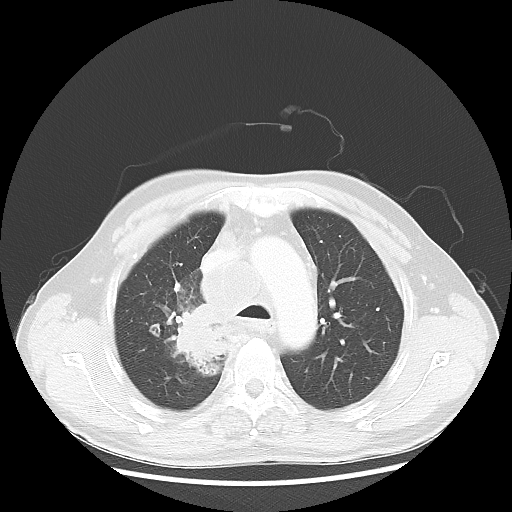
Chest CT, one axial slice; slice 42 of 60 in the series (ordered by position); reconstruction kernel LUNG; lung window (W 1500 / L -600 HU); 512 × 512 image matrix, field of view 382 × 382 mm. Patient: male, 64 years. From the clinical record (not read from this slice): clinical TNM (as recorded): T3 N3 M0.
Annotated regions visible in this slice (bounding box drawn by a radiologist):
- lung tumour (recorded histology: small cell carcinoma): bounding box <168,302,246,382> (left, top, right, bottom; pixels)